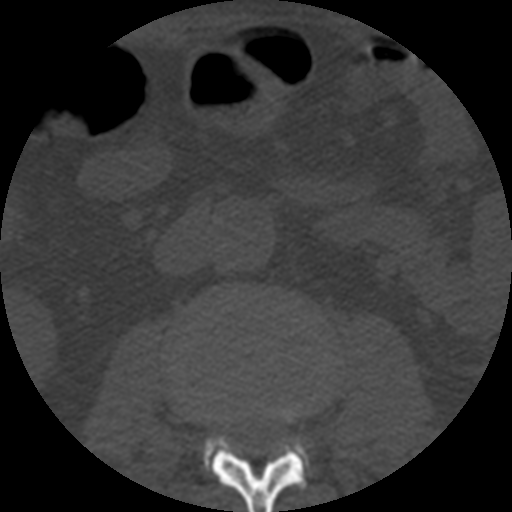
CT including the spine, one axial slice; position 140 of 508 along the scan axis; reconstruction kernel STANDARD; 120 kVp; bone window (W 1800 / L 400 HU); 1.25 mm slice thickness; 512 × 512 image matrix, field of view 160 × 160 mm. Patient age 57 years. Case-level facts recorded for this patient, not image findings: primary cancer: prostate.
Annotated regions visible in this slice (semi-automatic segmentation, software-assisted and operator-edited):
- L2 vertebra: box from (x=205, y=405) to (x=307, y=512) px
- L3 vertebra: (x=293, y=441)–(x=299, y=444)